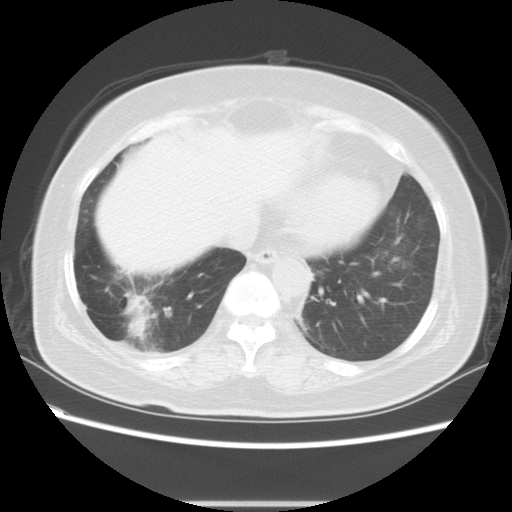
Chest CT, one axial slice; reconstruction kernel STANDARD; 120 kVp; lung window (W 1500 / L -600 HU); 5 mm slice thickness; 512 × 512 image matrix, field of view 350 × 350 mm. Patient: female, 65 years. Case-level facts recorded for this patient, not image findings: clinical TNM (as recorded): T2 N0 M1b.
Outlined on this slice (rectangle marked by the reading radiologist):
- lung tumour (recorded histology: adenocarcinoma): bounding box (x1, y1, x2, y2) in pixels: (126, 296, 155, 343)